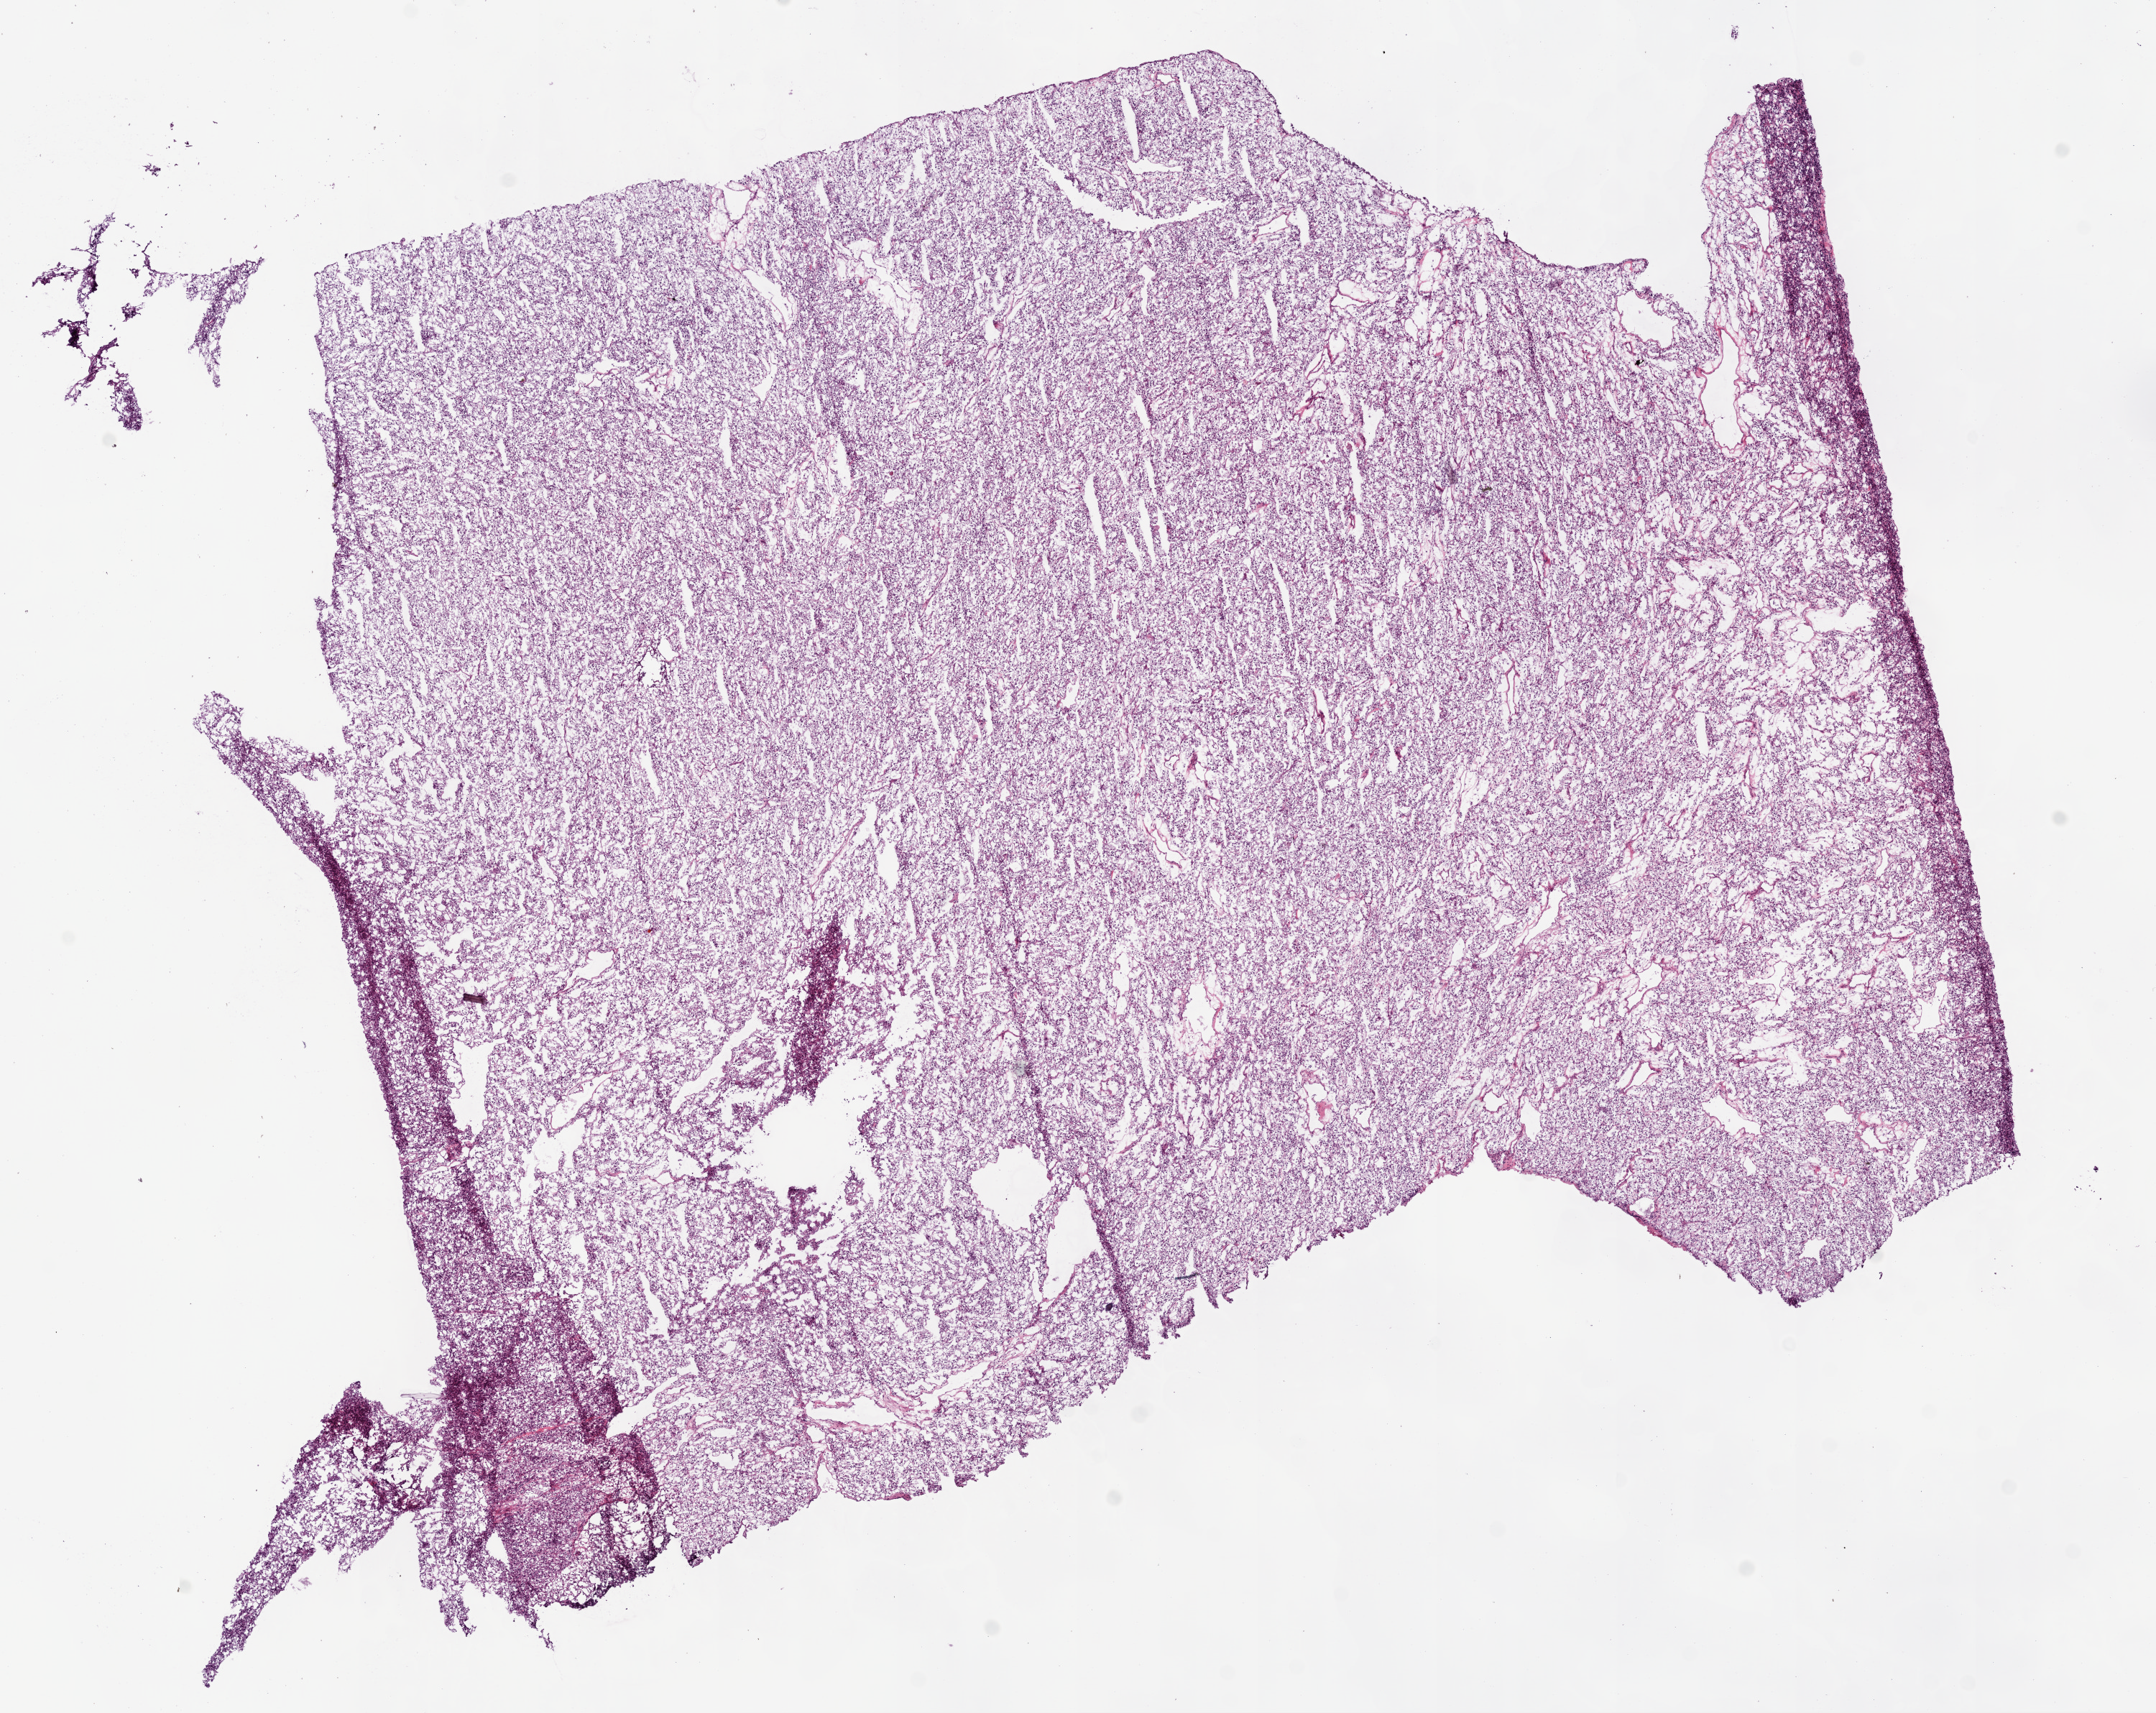
Digitized H&E-stained tissue section (whole slide), whole scanned area (about 12.0 x 9.6 mm) shown as a low-resolution overview. Frozen section. Primary tumour sample from the kidney. Patient: male, age at initial diagnosis 43 years.
Histologic diagnosis: Clear cell adenocarcinoma, NOS.